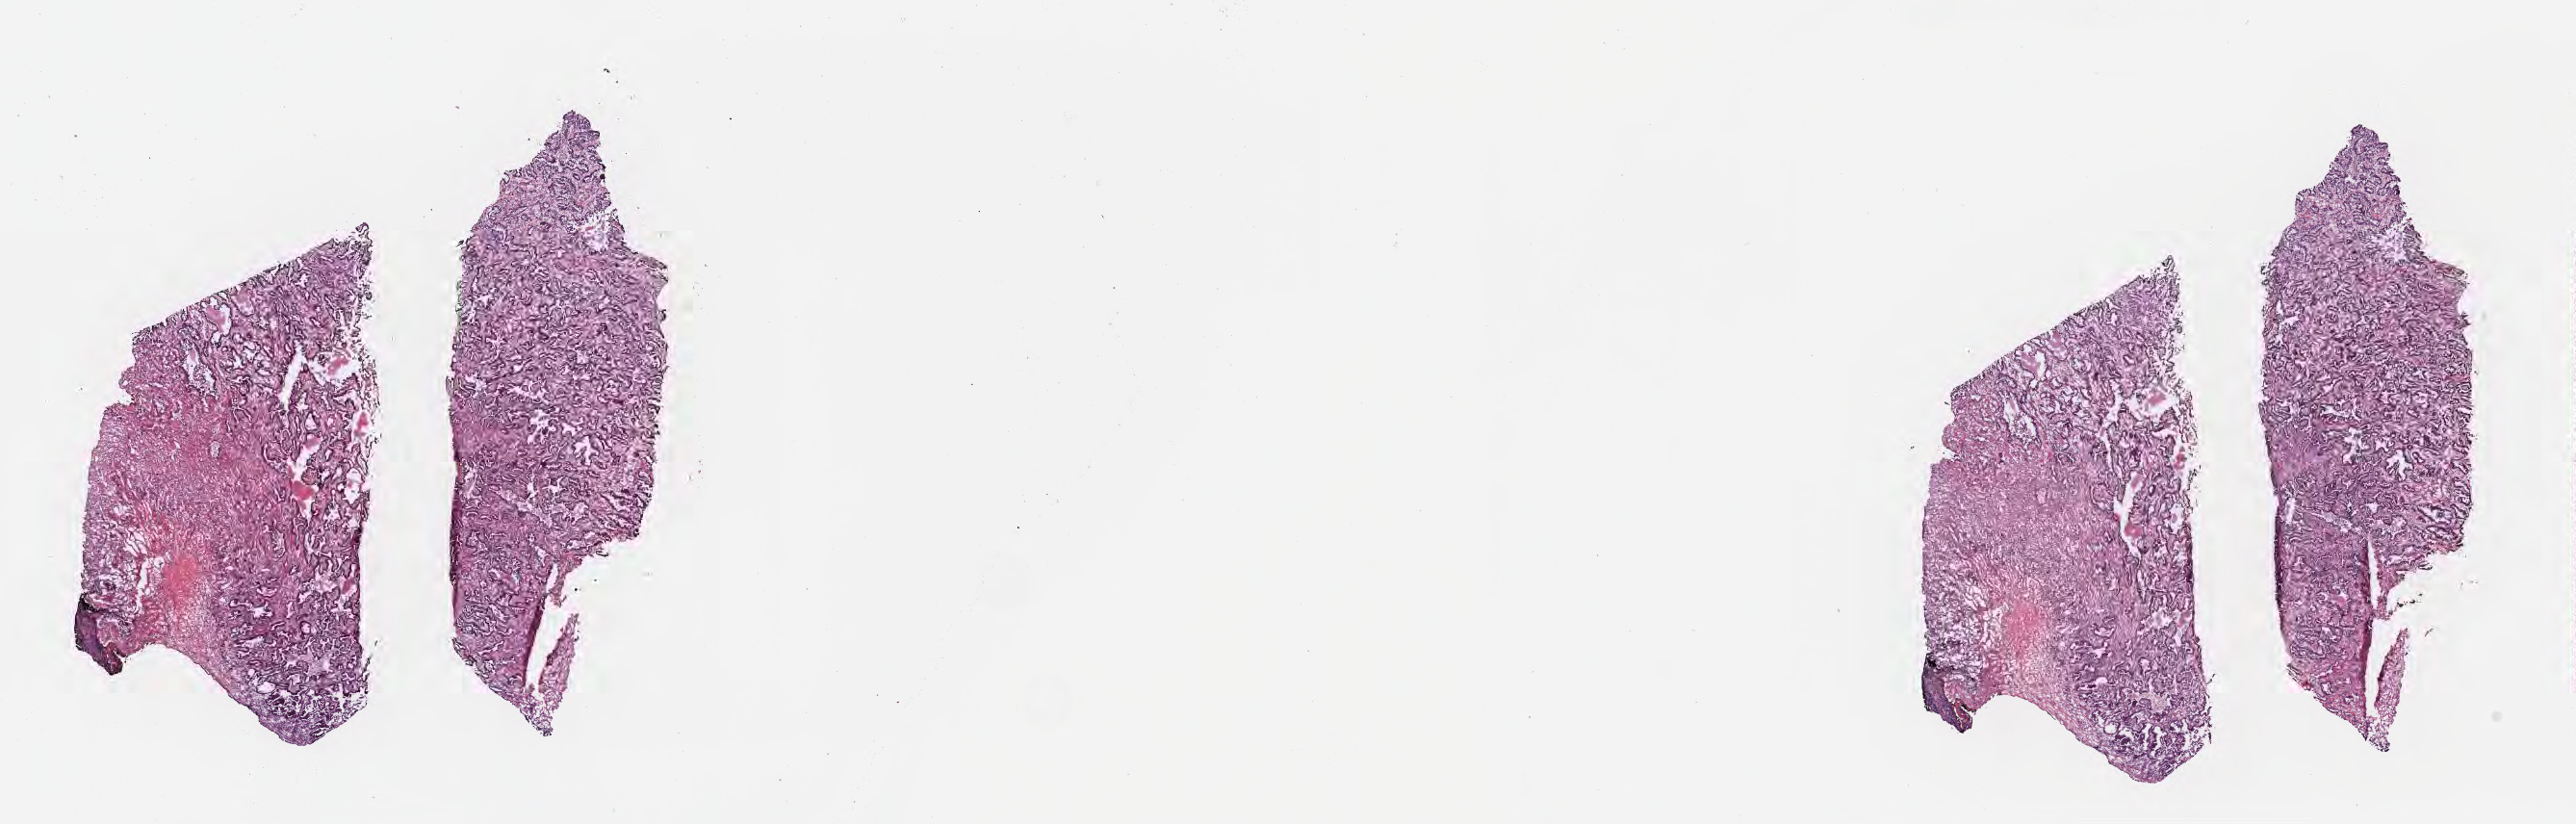
Whole-slide image, hematoxylin and eosin (H&E) stain, low-resolution overview of the scanned area, about 21.6 x 6.9 mm, cryosection, specimen: primary tumor, site: upper lobe of left lung. Patient male; age 60 years.
Diagnosis: Adenocarcinoma with mixed subtypes.